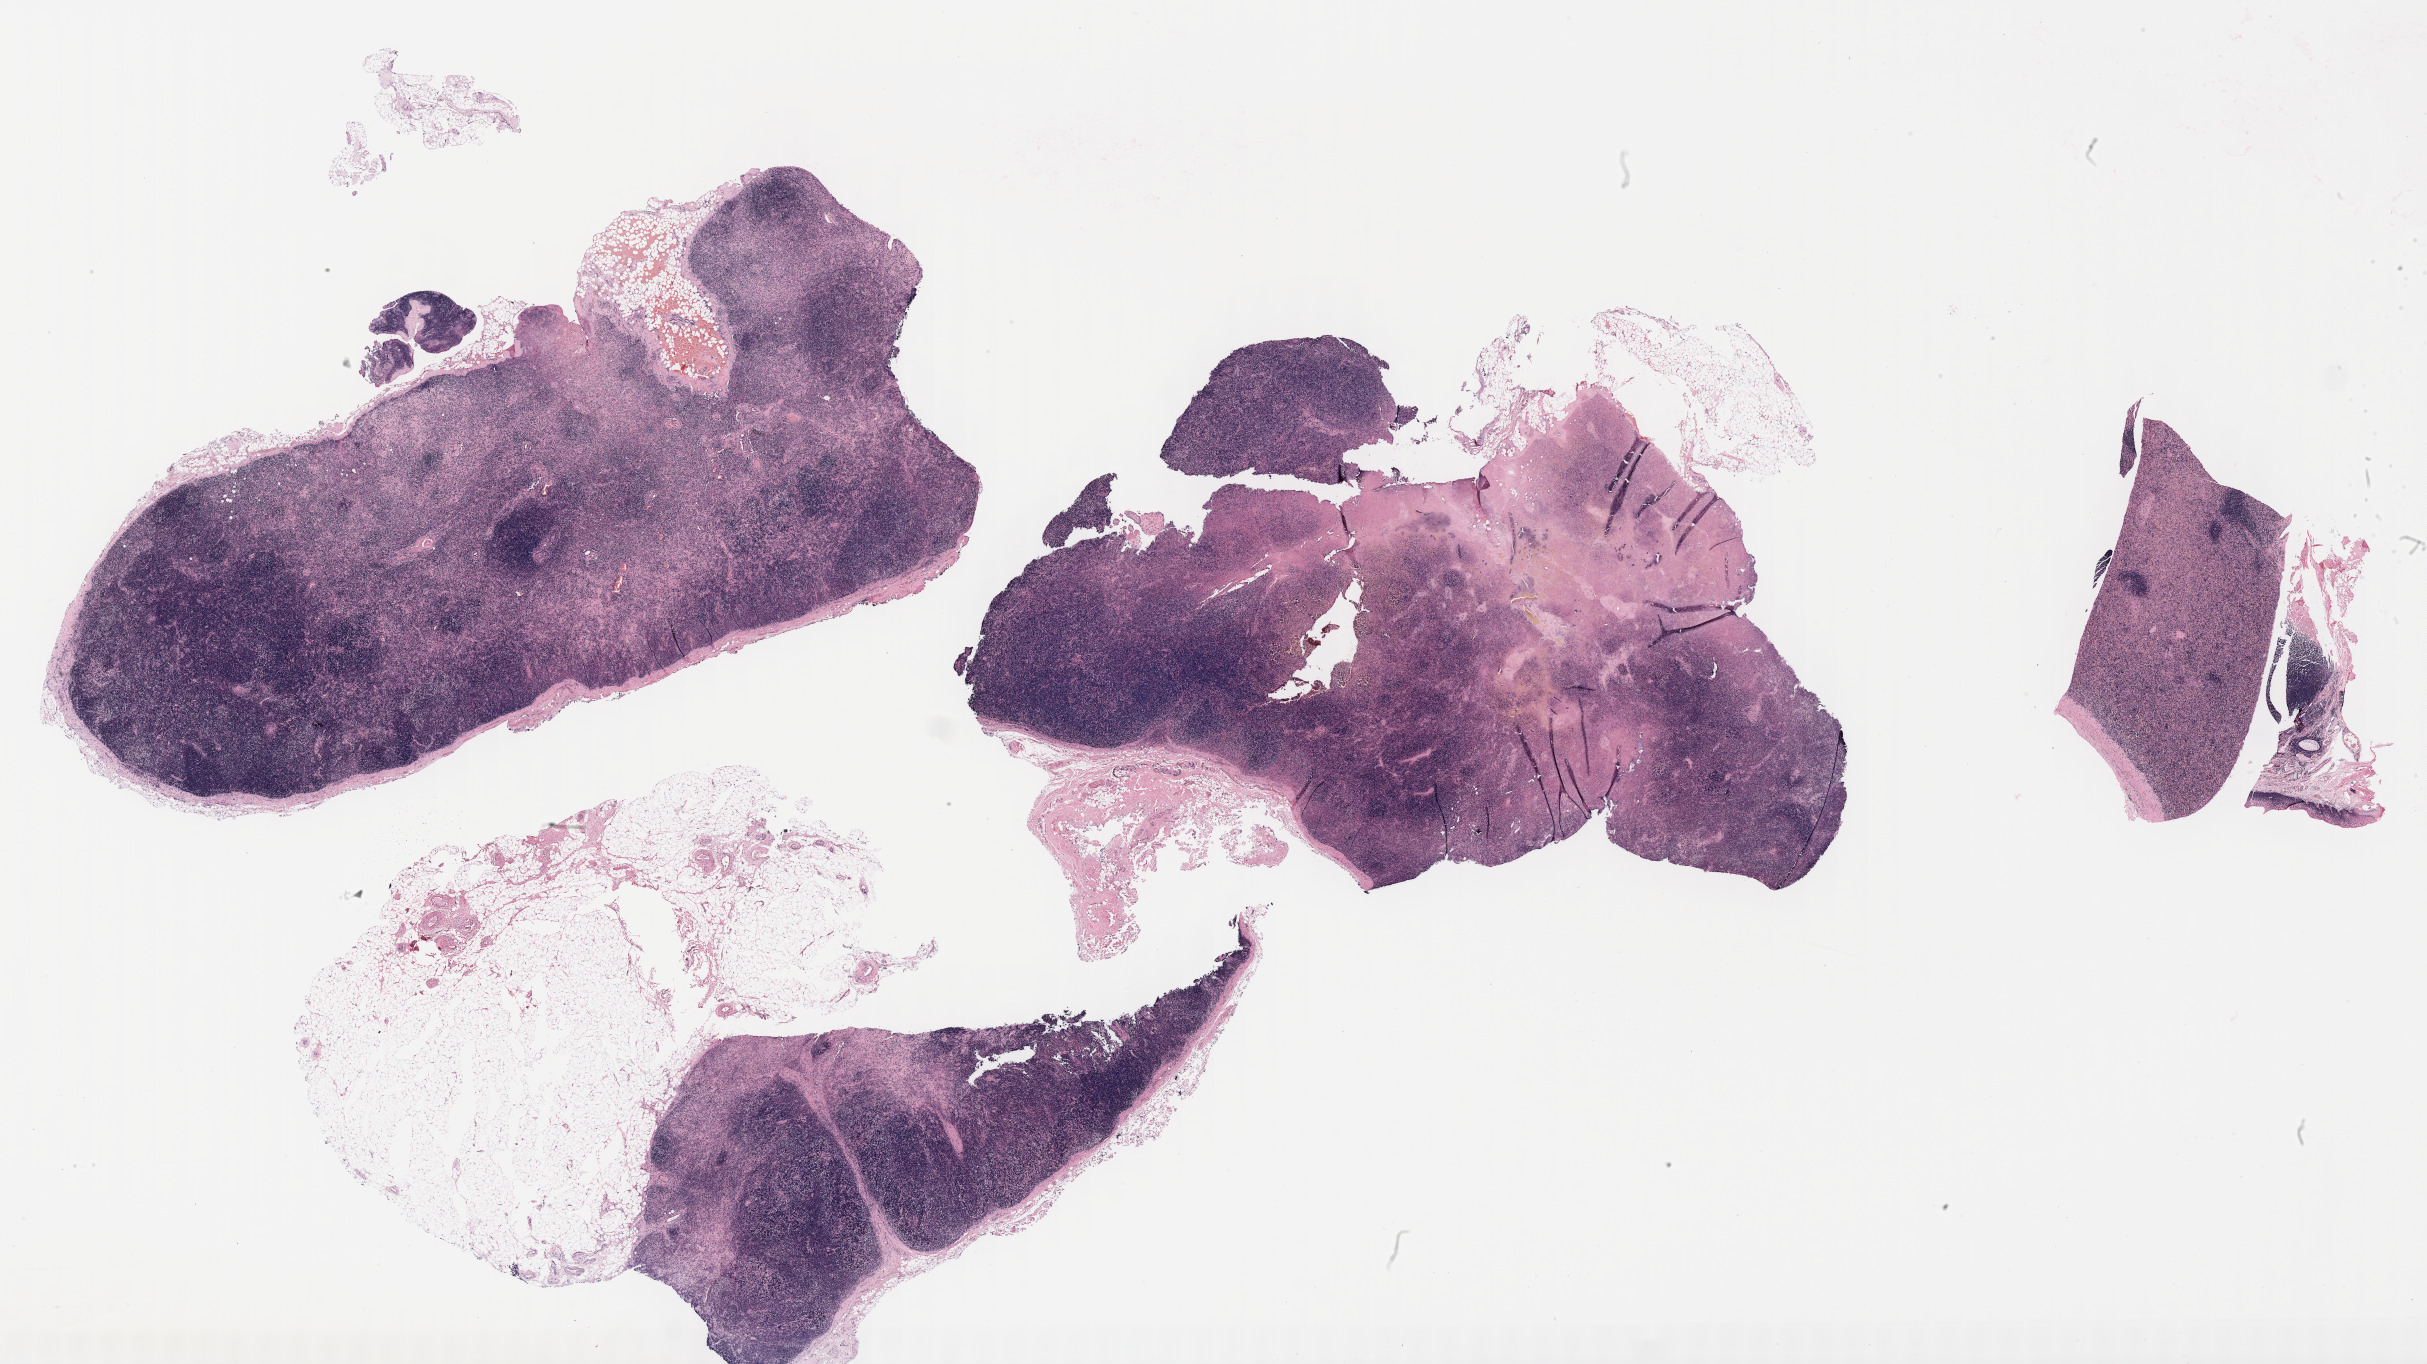
Whole-slide image; stain recorded as Iodonitrotetrazolium — low-resolution overview of the scanned area, about 39.2 x 22.1 mm. Specimen: tumor tissue. Anatomic site: lymph node. Patient male; aged 56.
• histologic diagnosis: Diffuse large B-cell lymphoma, NOS